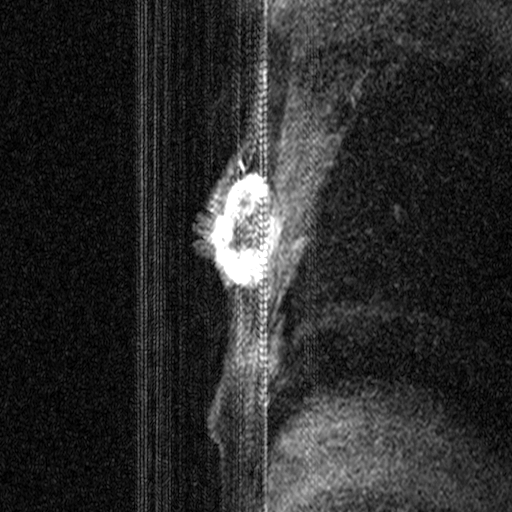
Breast MRI (dynamic contrast-enhanced), one sagittal slice. Position 26 of 44 along the scan axis. Dynamic contrast-enhanced study with each time point stored as its own series, time point 2 of 3 at this slice position (early post-contrast, ordered by acquisition time). 1.5 T. TE 4.5 ms, TR 11 ms. 3 mm slice thickness. 512 × 512 image matrix, field of view 200 × 200 mm. Female patient, age 44 years. Case-level facts recorded for this patient, not image findings: setting: breast cancer imaged before/during neoadjuvant chemotherapy; receptor status: HR-positive, HER2-negative.
Annotated regions visible in this slice (semi-automatically segmented with operator editing):
- analysis volume of interest (the breast-tissue region the enhancement analysis was run in; not a lesion): bounding box <206,164,278,299> (left, top, right, bottom; pixels)
- tumour enhancement mask (voxels above the 90 % enhancement threshold inside the analysis volume of interest): <208,164,278,297>